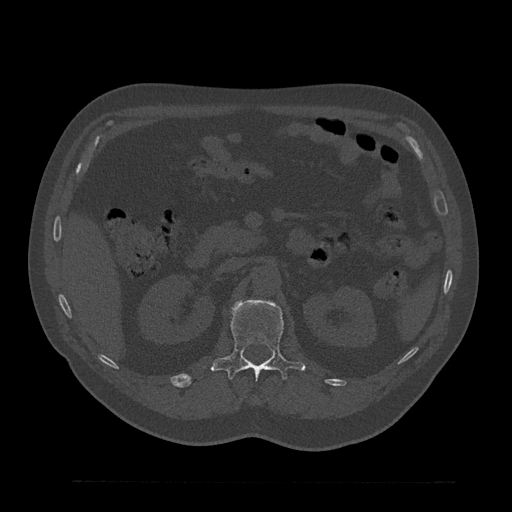
CT including the spine, one axial slice; slice 168 of 797 in the series (ordered by position); bone window (W 1800 / L 400 HU); 0.5 mm slice thickness; 512 × 512 image matrix. Patient: male, 61 years. Case-level facts recorded for this patient, not image findings: primary cancer: prostate.
Structures marked on this image (semi-automatic segmentation, software-assisted and operator-edited):
- L1 vertebra: bounding box [x1, y1, x2, y2] px = [211, 299, 305, 380]